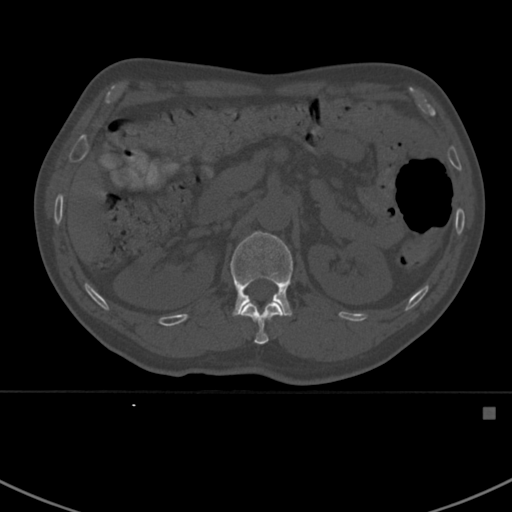
CT including the spine, one axial slice. Bone window (W 1800 / L 400 HU). 512 × 512 image matrix. Male patient, age 59 years. From the clinical record (not read from this slice): primary cancer: prostate.
Annotated regions visible in this slice (semi-automatic segmentation, software-assisted and operator-edited):
- L1 vertebra: box from (x=230, y=231) to (x=310, y=317) px
- T12 vertebra: (x=242, y=302)–(x=281, y=345)